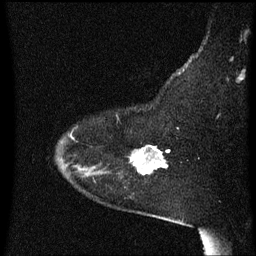
Breast MRI (dynamic contrast-enhanced), one sagittal slice. Position 46 of 60 along the scan axis. Dynamic contrast-enhanced series, image 2 of 3 at this slice position (ordered by acquisition). 1.5 T. TE 4.2 ms, TR 8.4 ms. 2 mm slice thickness. 256 × 256 image matrix. Patient: female, 54 years. From the clinical record (not read from this slice): setting: breast cancer imaged before/during neoadjuvant chemotherapy; receptor status: HR-positive, HER2-negative.
Structures marked on this image (semi-automatically segmented with operator editing):
- analysis volume of interest (the breast-tissue region the enhancement analysis was run in; not a lesion): box from (x=120, y=146) to (x=171, y=177) px
- tumour enhancement mask (voxels above the 70 % enhancement threshold inside the analysis volume of interest): (x=132, y=148)–(x=169, y=175)